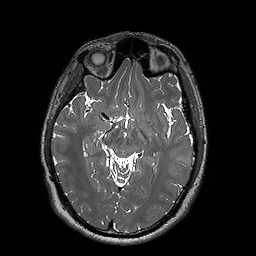
Brain MRI from a brain-tumour surgery series, one axial slice. Slice 98 of 192 in the series (ordered by position). 1 mm slice thickness. 256 × 256 image matrix, field of view 250 × 250 mm. Case-level facts recorded for this patient, not image findings: histopathology: Oligodendroglioma; WHO grade: 2; IDH mutation: yes; tumour location: Left Posterior Temporal.
Structures marked on this image (outlined manually by an expert reader):
- tumour: bounding box [x1, y1, x2, y2] px = [167, 156, 186, 172]